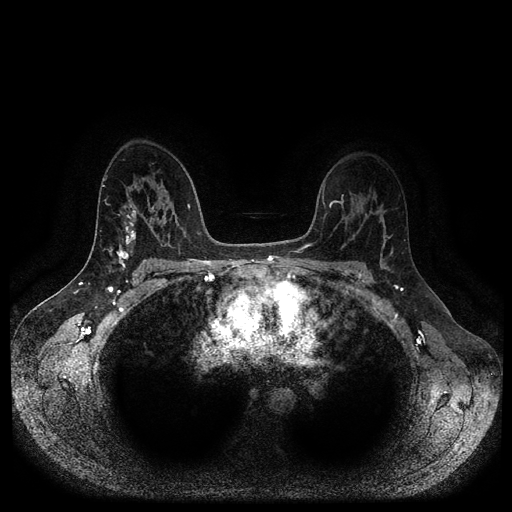
Breast MRI (dynamic contrast-enhanced, multi-phase), one axial slice; slice 66 of 116 in the series (ordered by position); dynamic contrast-enhanced series, time point 2 of 5 at this slice position (early post-contrast); 1.5 T; TE 2.6 ms, TR 5.3 ms; 2 mm slice thickness; 512 × 512 image matrix, field of view 360 × 360 mm. Female patient, age 45 years.
Annotated regions visible in this slice (semi-automatic segmentation, software-assisted and operator-edited):
- breast lesion (labelled benign in the annotation): bounding box [x1, y1, x2, y2] px = [121, 215, 136, 245]
- breast lesion (labelled 'tumour' in the annotation; benign lesions carry a separate 'benign' label): [116, 249, 133, 272]